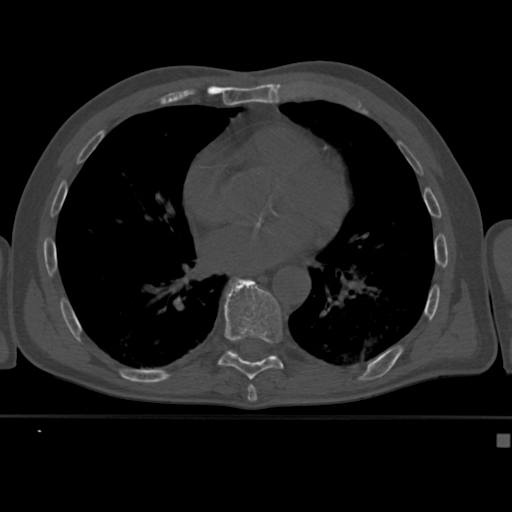
CT including the spine, one axial slice; slice 245 of 430 in the series (ordered by position); reconstruction kernel Br40s; bone window (W 1800 / L 400 HU); 1.5 mm slice thickness; 512 × 512 image matrix. Patient: male, 64 years. From the clinical record (not read from this slice): primary cancer: uterus.
Annotated regions visible in this slice (semi-automatically segmented with operator editing):
- T9 vertebra: bounding box (x1, y1, x2, y2) in pixels: (218, 278, 284, 380)